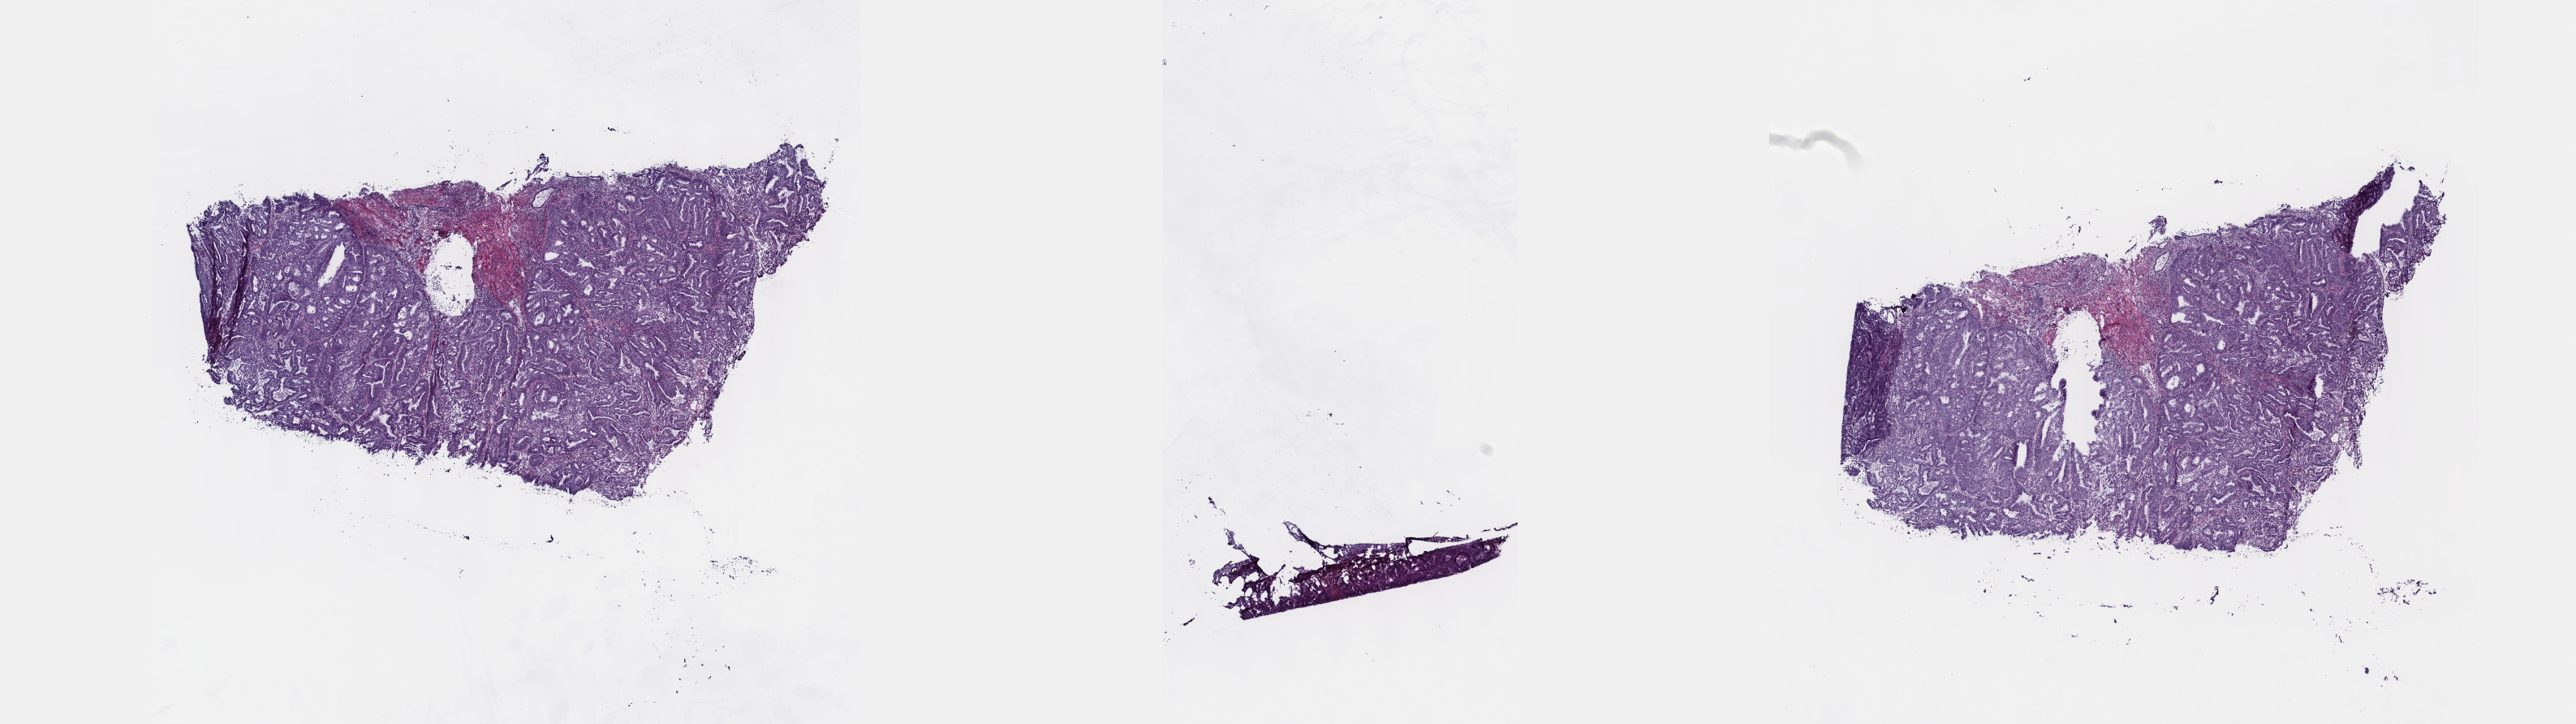
Whole-slide histology image, H&E — shown as a low-resolution overview of the whole scanned area (about 25.7 x 7.2 mm), frozen section from the top of the tissue portion, primary tumour sample from the uterus. Female patient; age at initial diagnosis 54 years. Histologic grade: G1 (well differentiated). Pathologist review of this section (percent, as recorded): tumour cells 80%, tumour nuclei 80%, normal cells 0%, stromal cells 15%, necrosis 5%. Inflammatory infiltration, as recorded: lymphocyte infiltration 40%, monocyte infiltration 20%, neutrophil infiltration 20%.
• pathologic diagnosis: Endometrioid adenocarcinoma, NOS (endometrium)
• FIGO stage: I